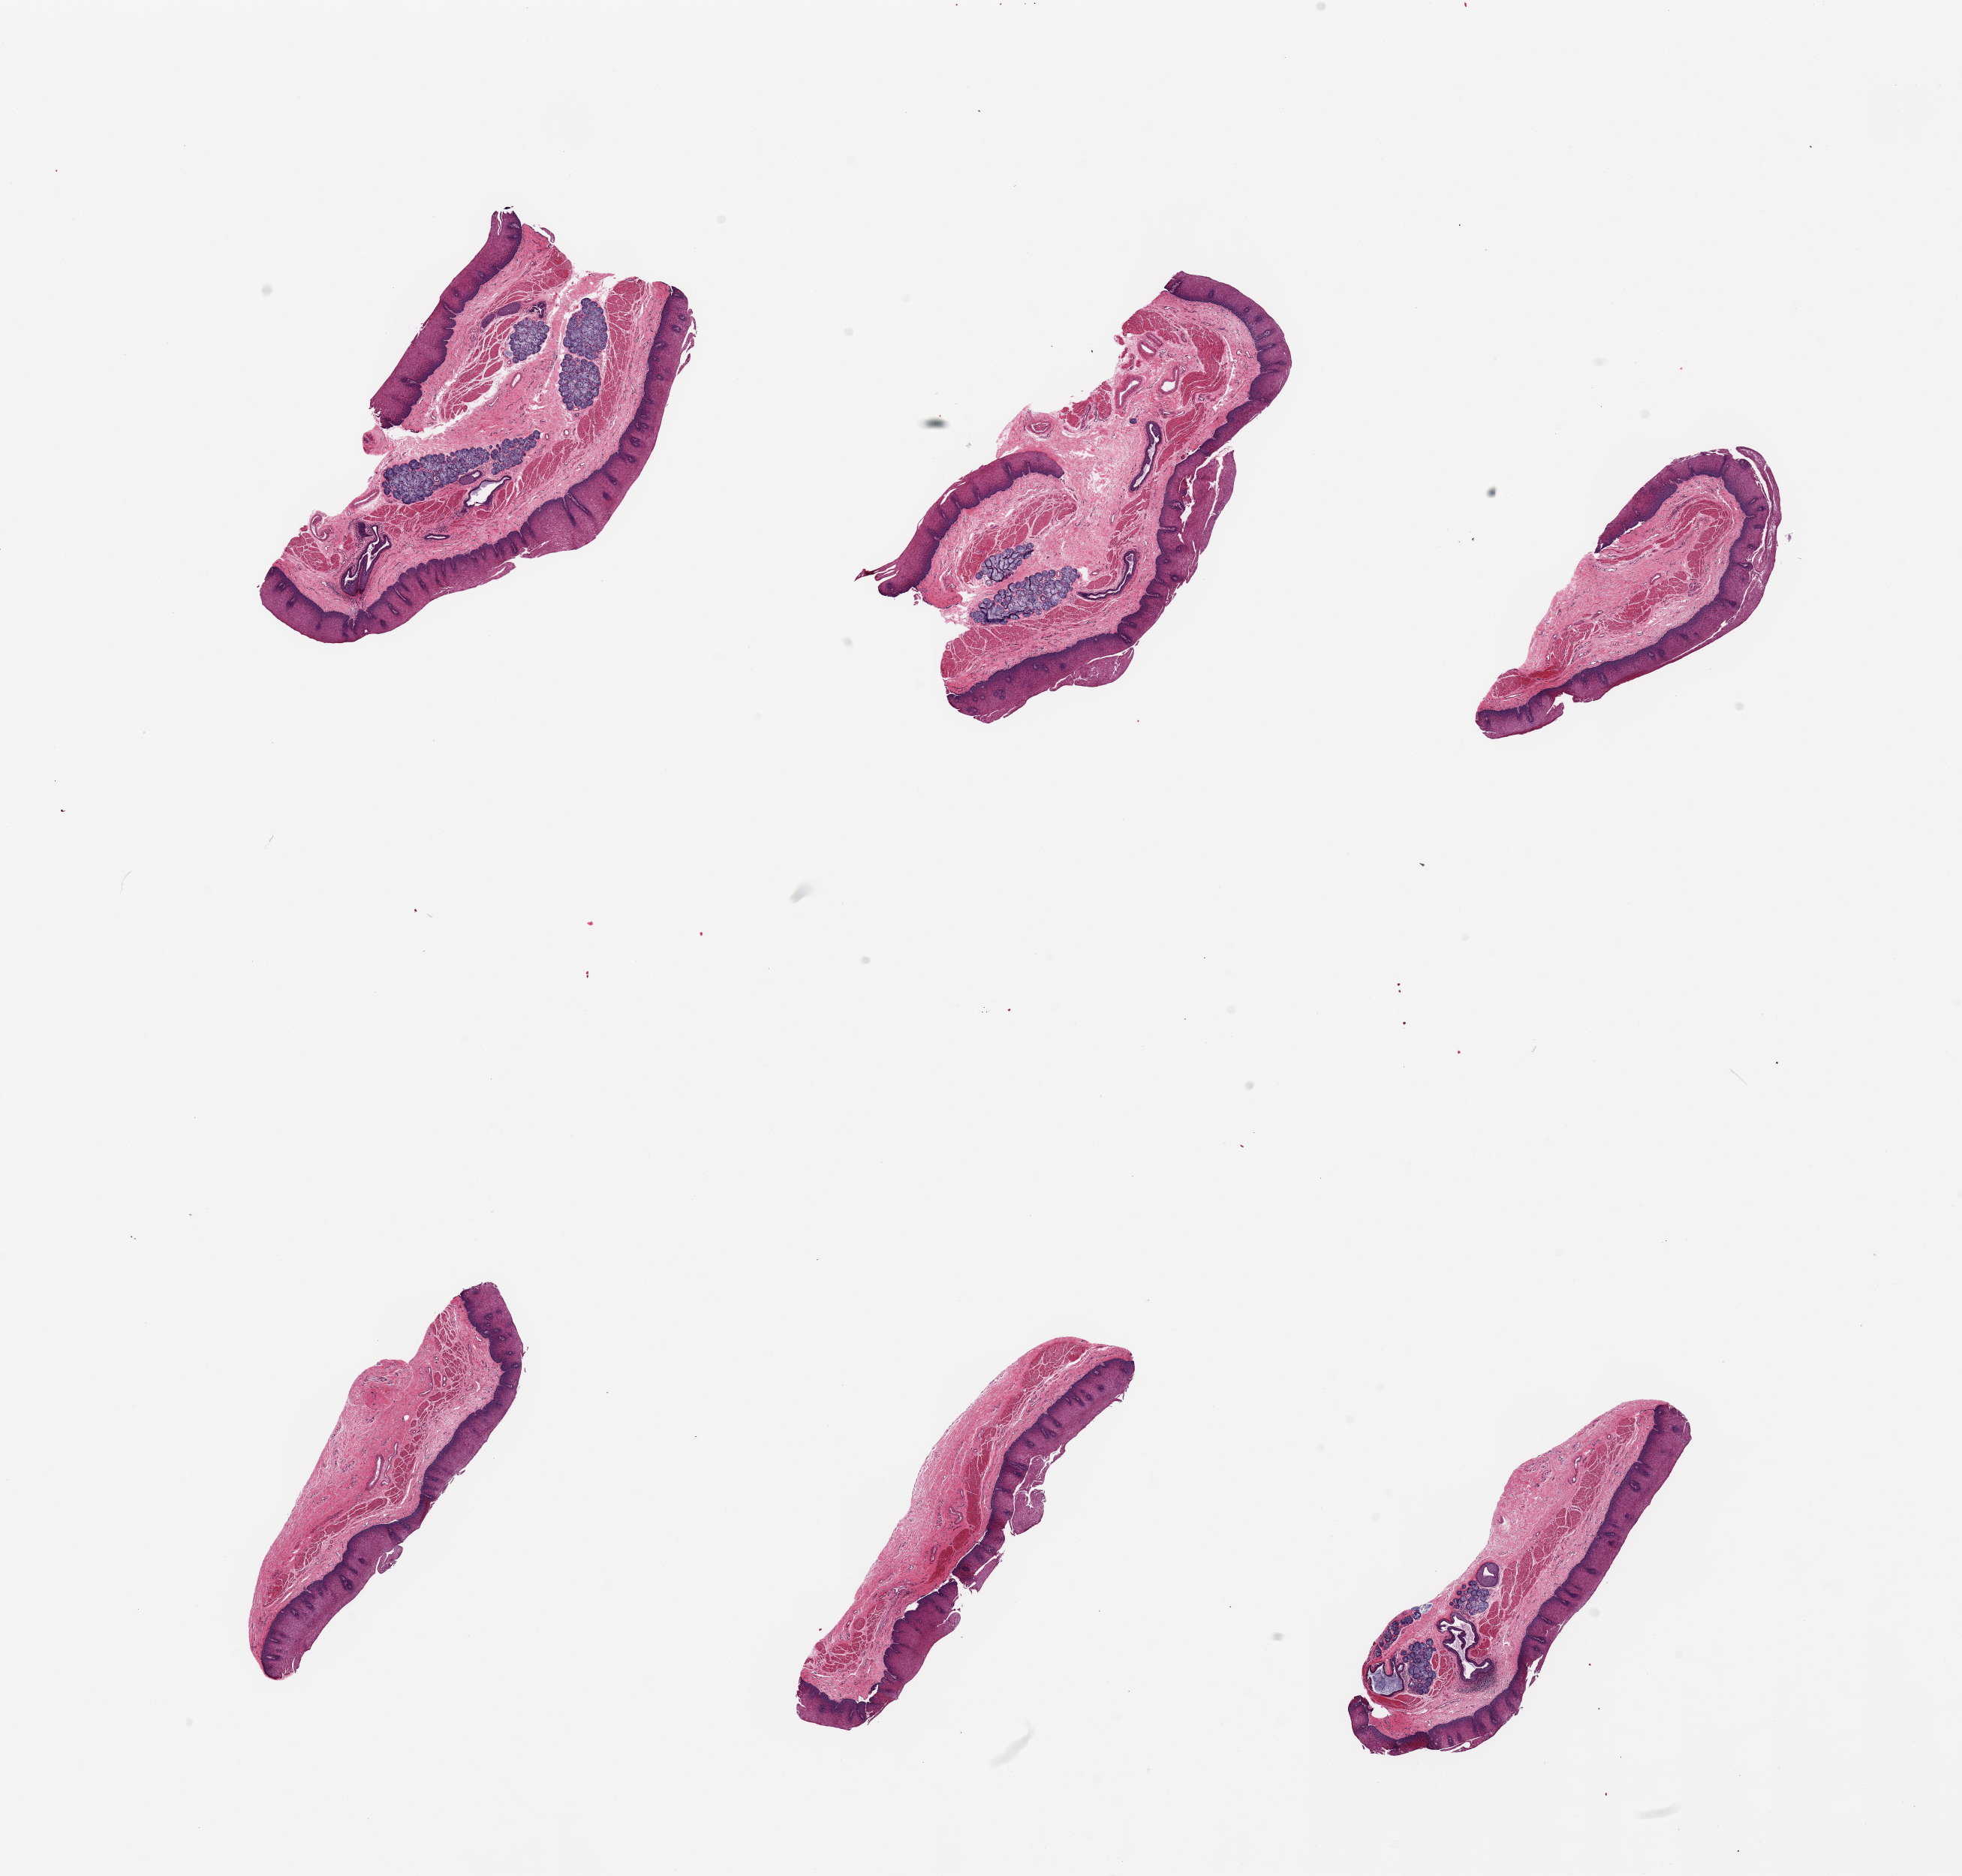
Digitized haematoxylin and eosin-stained section, shown as a low-resolution overview of the whole scanned area (about 20.7 x 19.8 mm, slide scanned at 20x), PAXgene-fixed paraffin-embedded (PFPE) section, section of esophageal mucous membrane (target tissue), donor tissue sample. Donor: male.
Pathologist's review note for this sample: 6 pieces; several submucosal glands; ~400 microns stratified squamous epithelium.